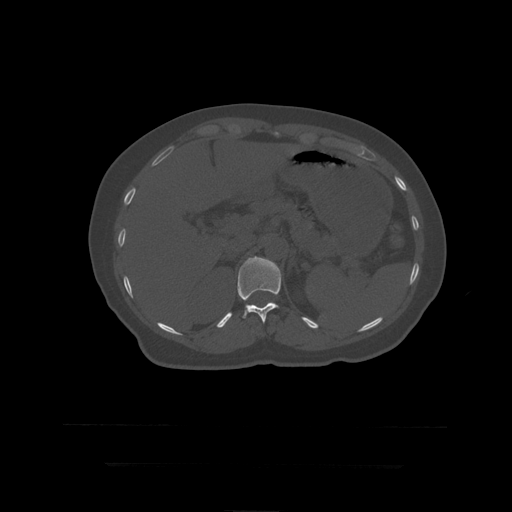
CT including the spine, one axial slice. Position 196 of 399 along the scan axis. Reconstruction kernel STANDARD. 120 kVp. Bone window (W 1800 / L 400 HU). 512 × 512 image matrix, field of view 450 × 450 mm. Patient age 41 years. Case-level facts recorded for this patient, not image findings: primary cancer: breast.
Outlined on this slice (semi-automatic segmentation, software-assisted and operator-edited):
- T12 vertebra: bounding box (x1, y1, x2, y2) in pixels: (238, 256, 281, 324)